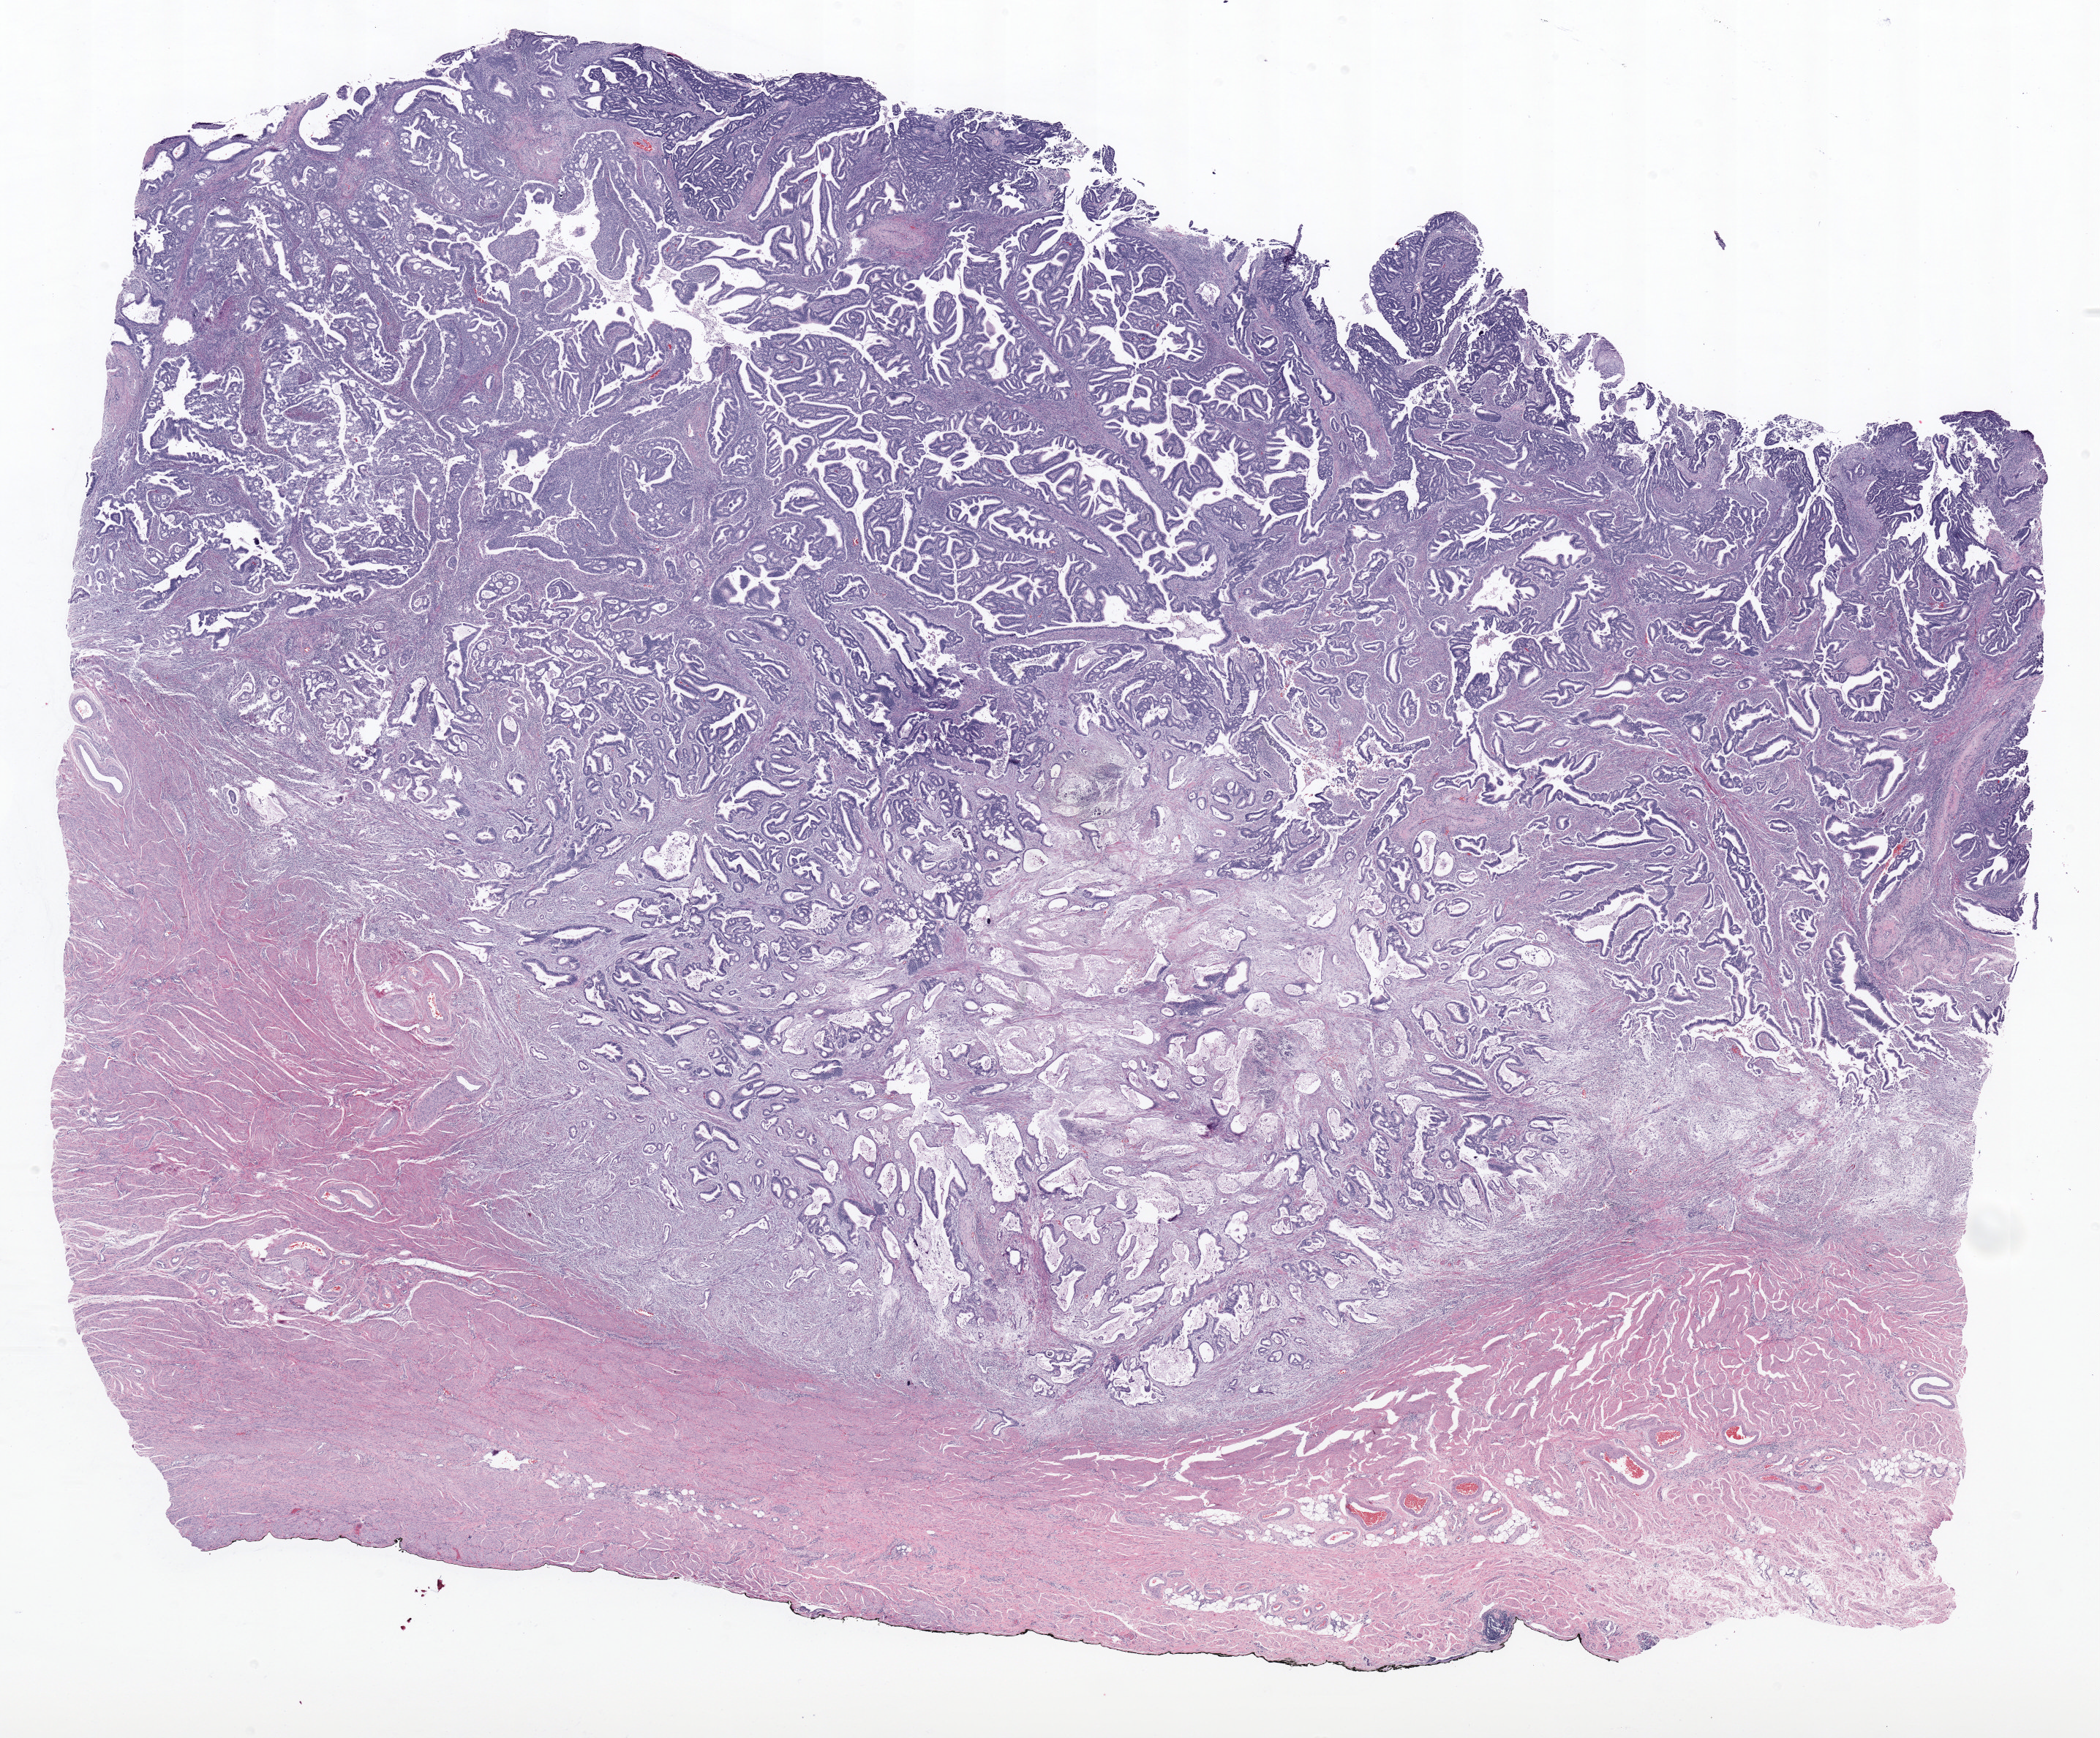
H&E-stained whole-slide image — a low-resolution overview of the entire scanned area, about 22.9 x 18.9 mm (slide scanned at 20x). Formalin-fixed paraffin-embedded (FFPE) diagnostic section. Primary tumour sample from the cervix. Patient: female, age at initial diagnosis 48 years. Histologic grade: G2 (moderately differentiated).
Histologic diagnosis: Adenocarcinoma, endocervical type. Lymph nodes positive (case pathology): 1 of 25 examined. FIGO stage: IVB.